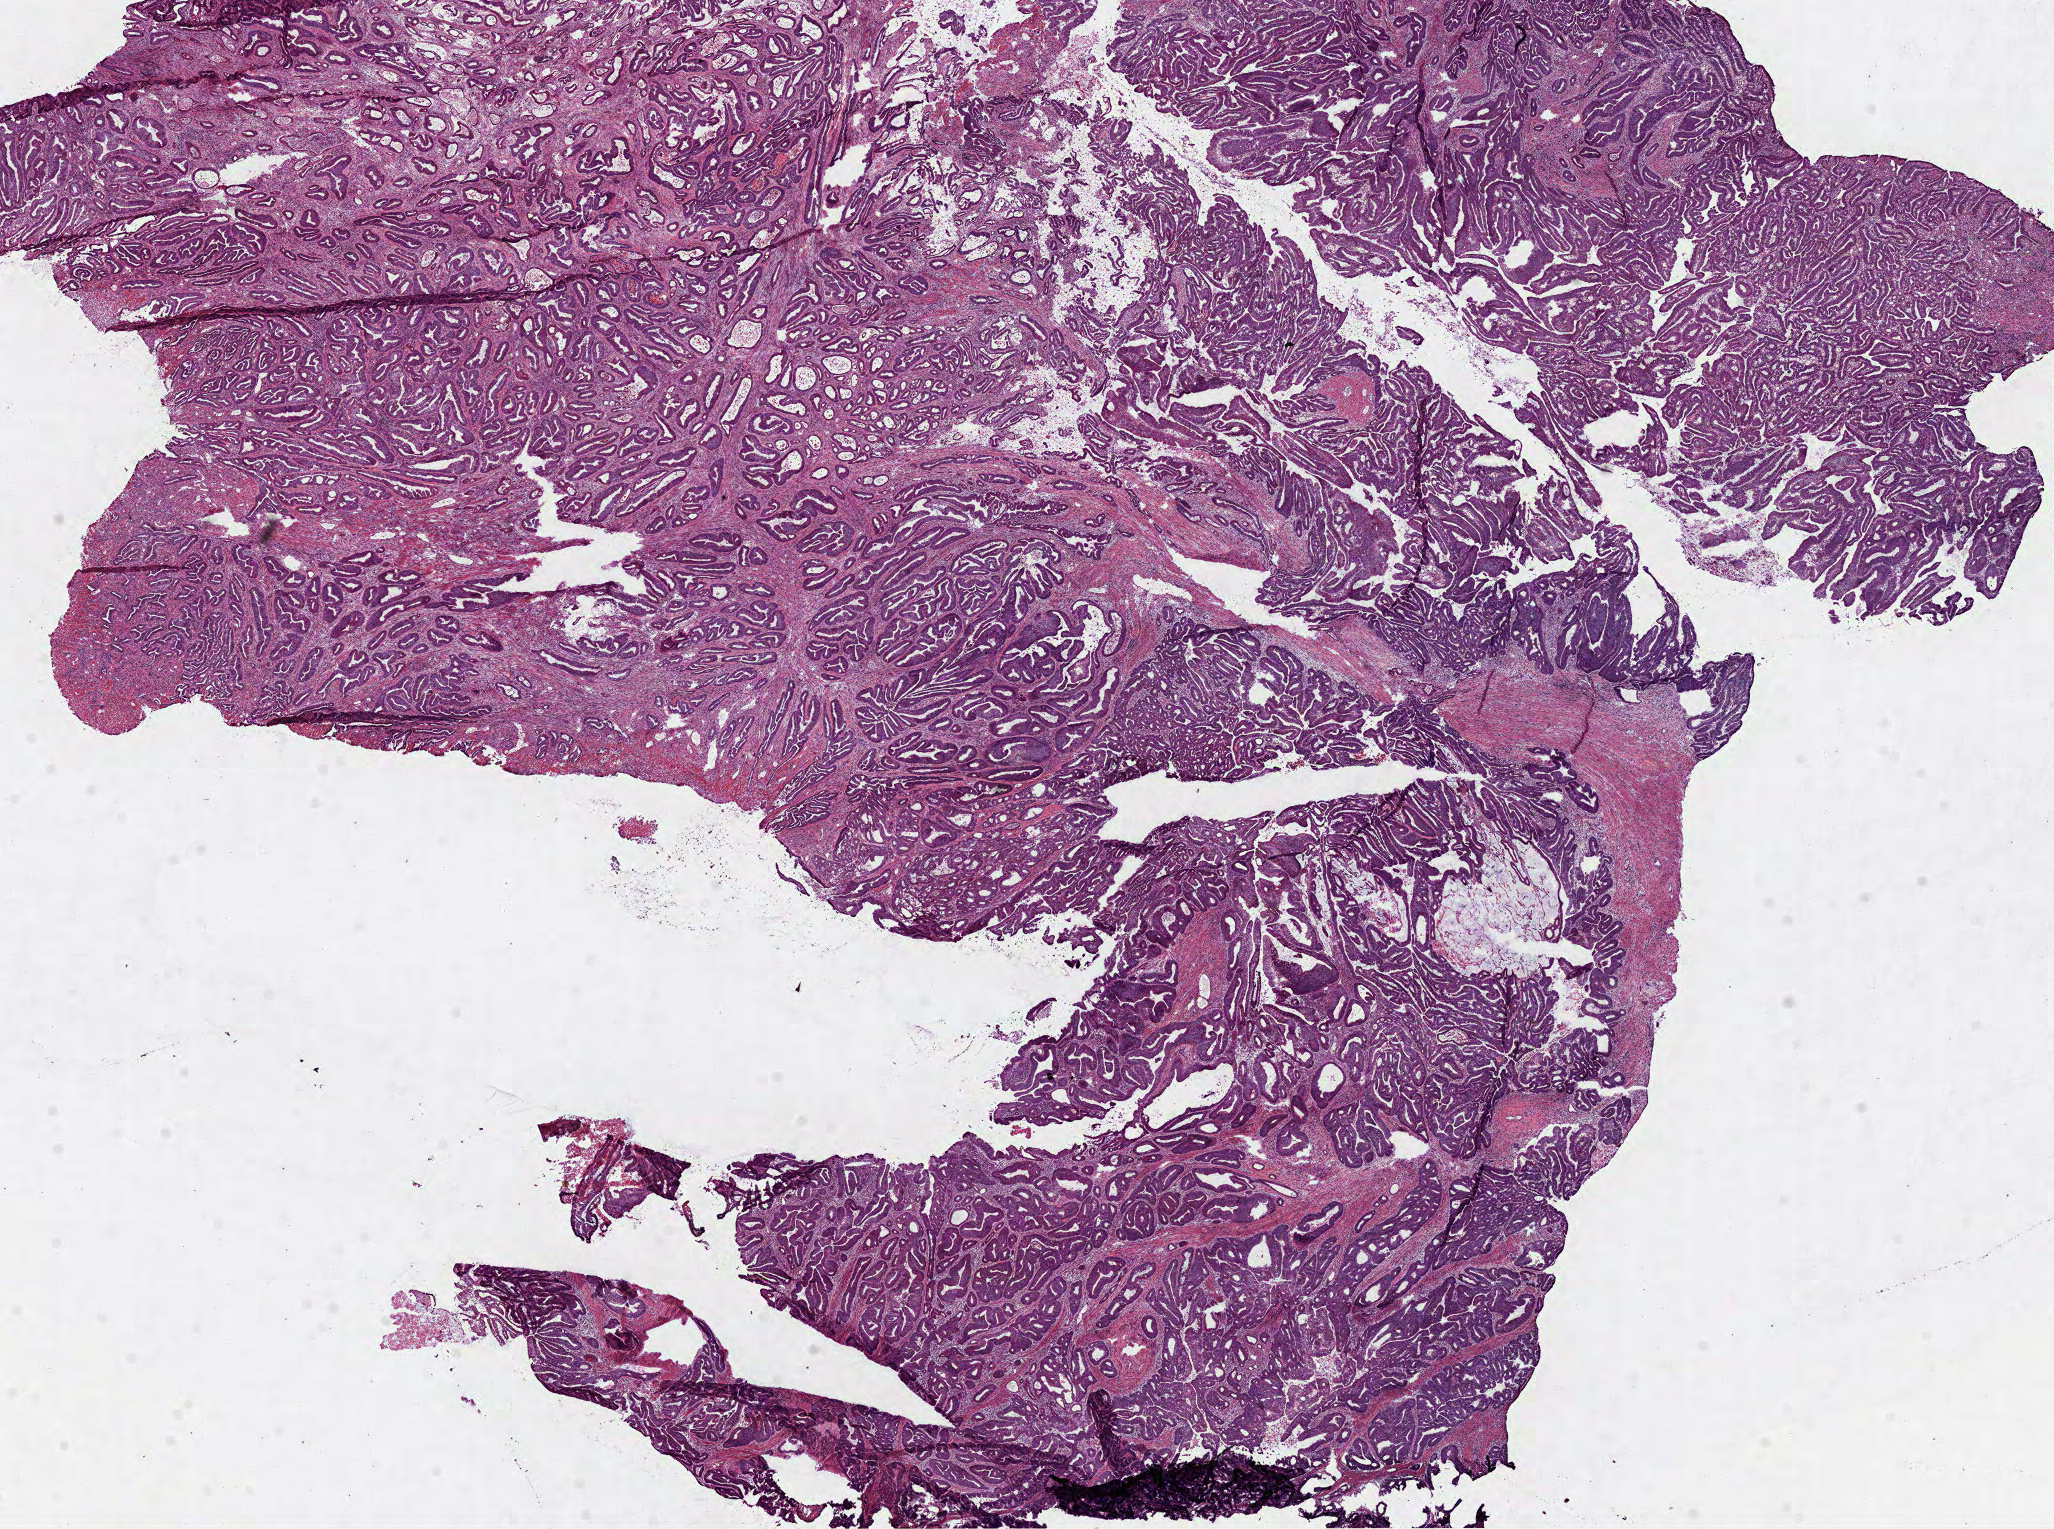
Hematoxylin and eosin (H&E) stained whole-slide image — a low-resolution overview of the entire scanned area, about 16.6 x 12.3 mm. Frozen section from the bottom of the tissue portion. Colon, primary tumour sample. Female, age 63 years at initial diagnosis. Pathologist review of this section (percent, as recorded): tumour cells 80%, tumour nuclei 80%, normal cells 0%, stromal cells 12%, necrosis 8%.
AJCC pathologic stage: IVA (7th edition). Lymph nodes positive (case pathology): 0 of 19 examined. Diagnosis: Adenocarcinoma, NOS (sigmoid colon).